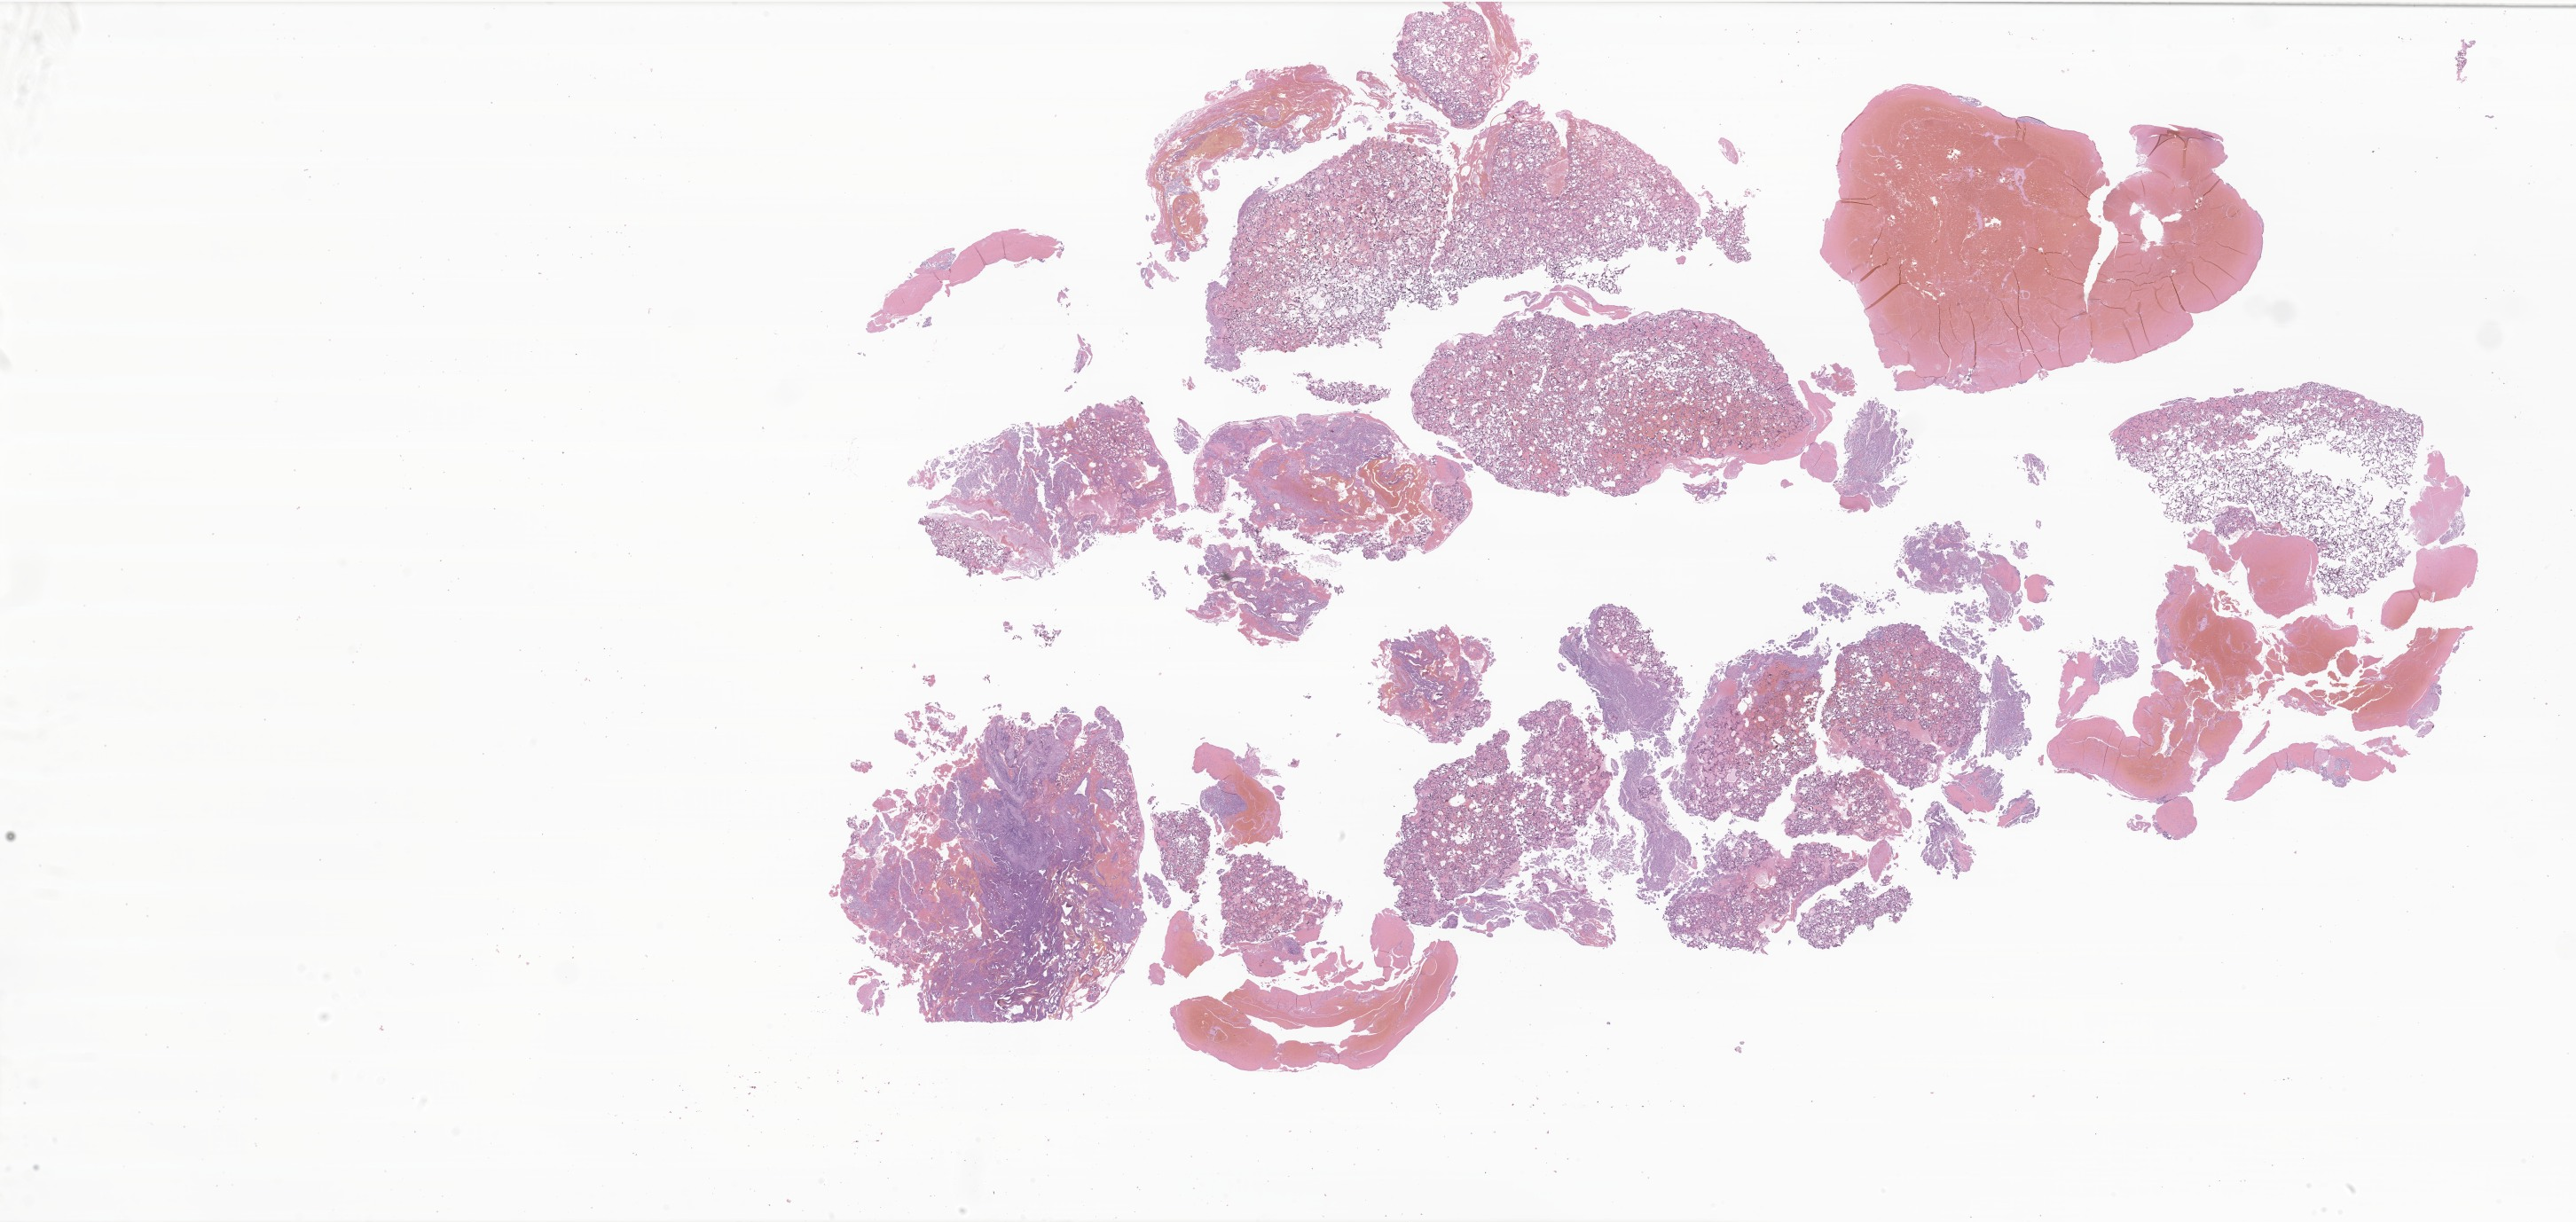
H&E whole-slide image of tumor tissue from the cerebral ventricle — low-resolution overview of the scanned area, about 49.0 x 23.2 mm, formalin-fixed, paraffin-embedded (FFPE) tissue. Patient male; age 457 days (about 1.3 years).
Diagnosis (ICD-O-3 morphology term): Choroid plexus carcinoma.